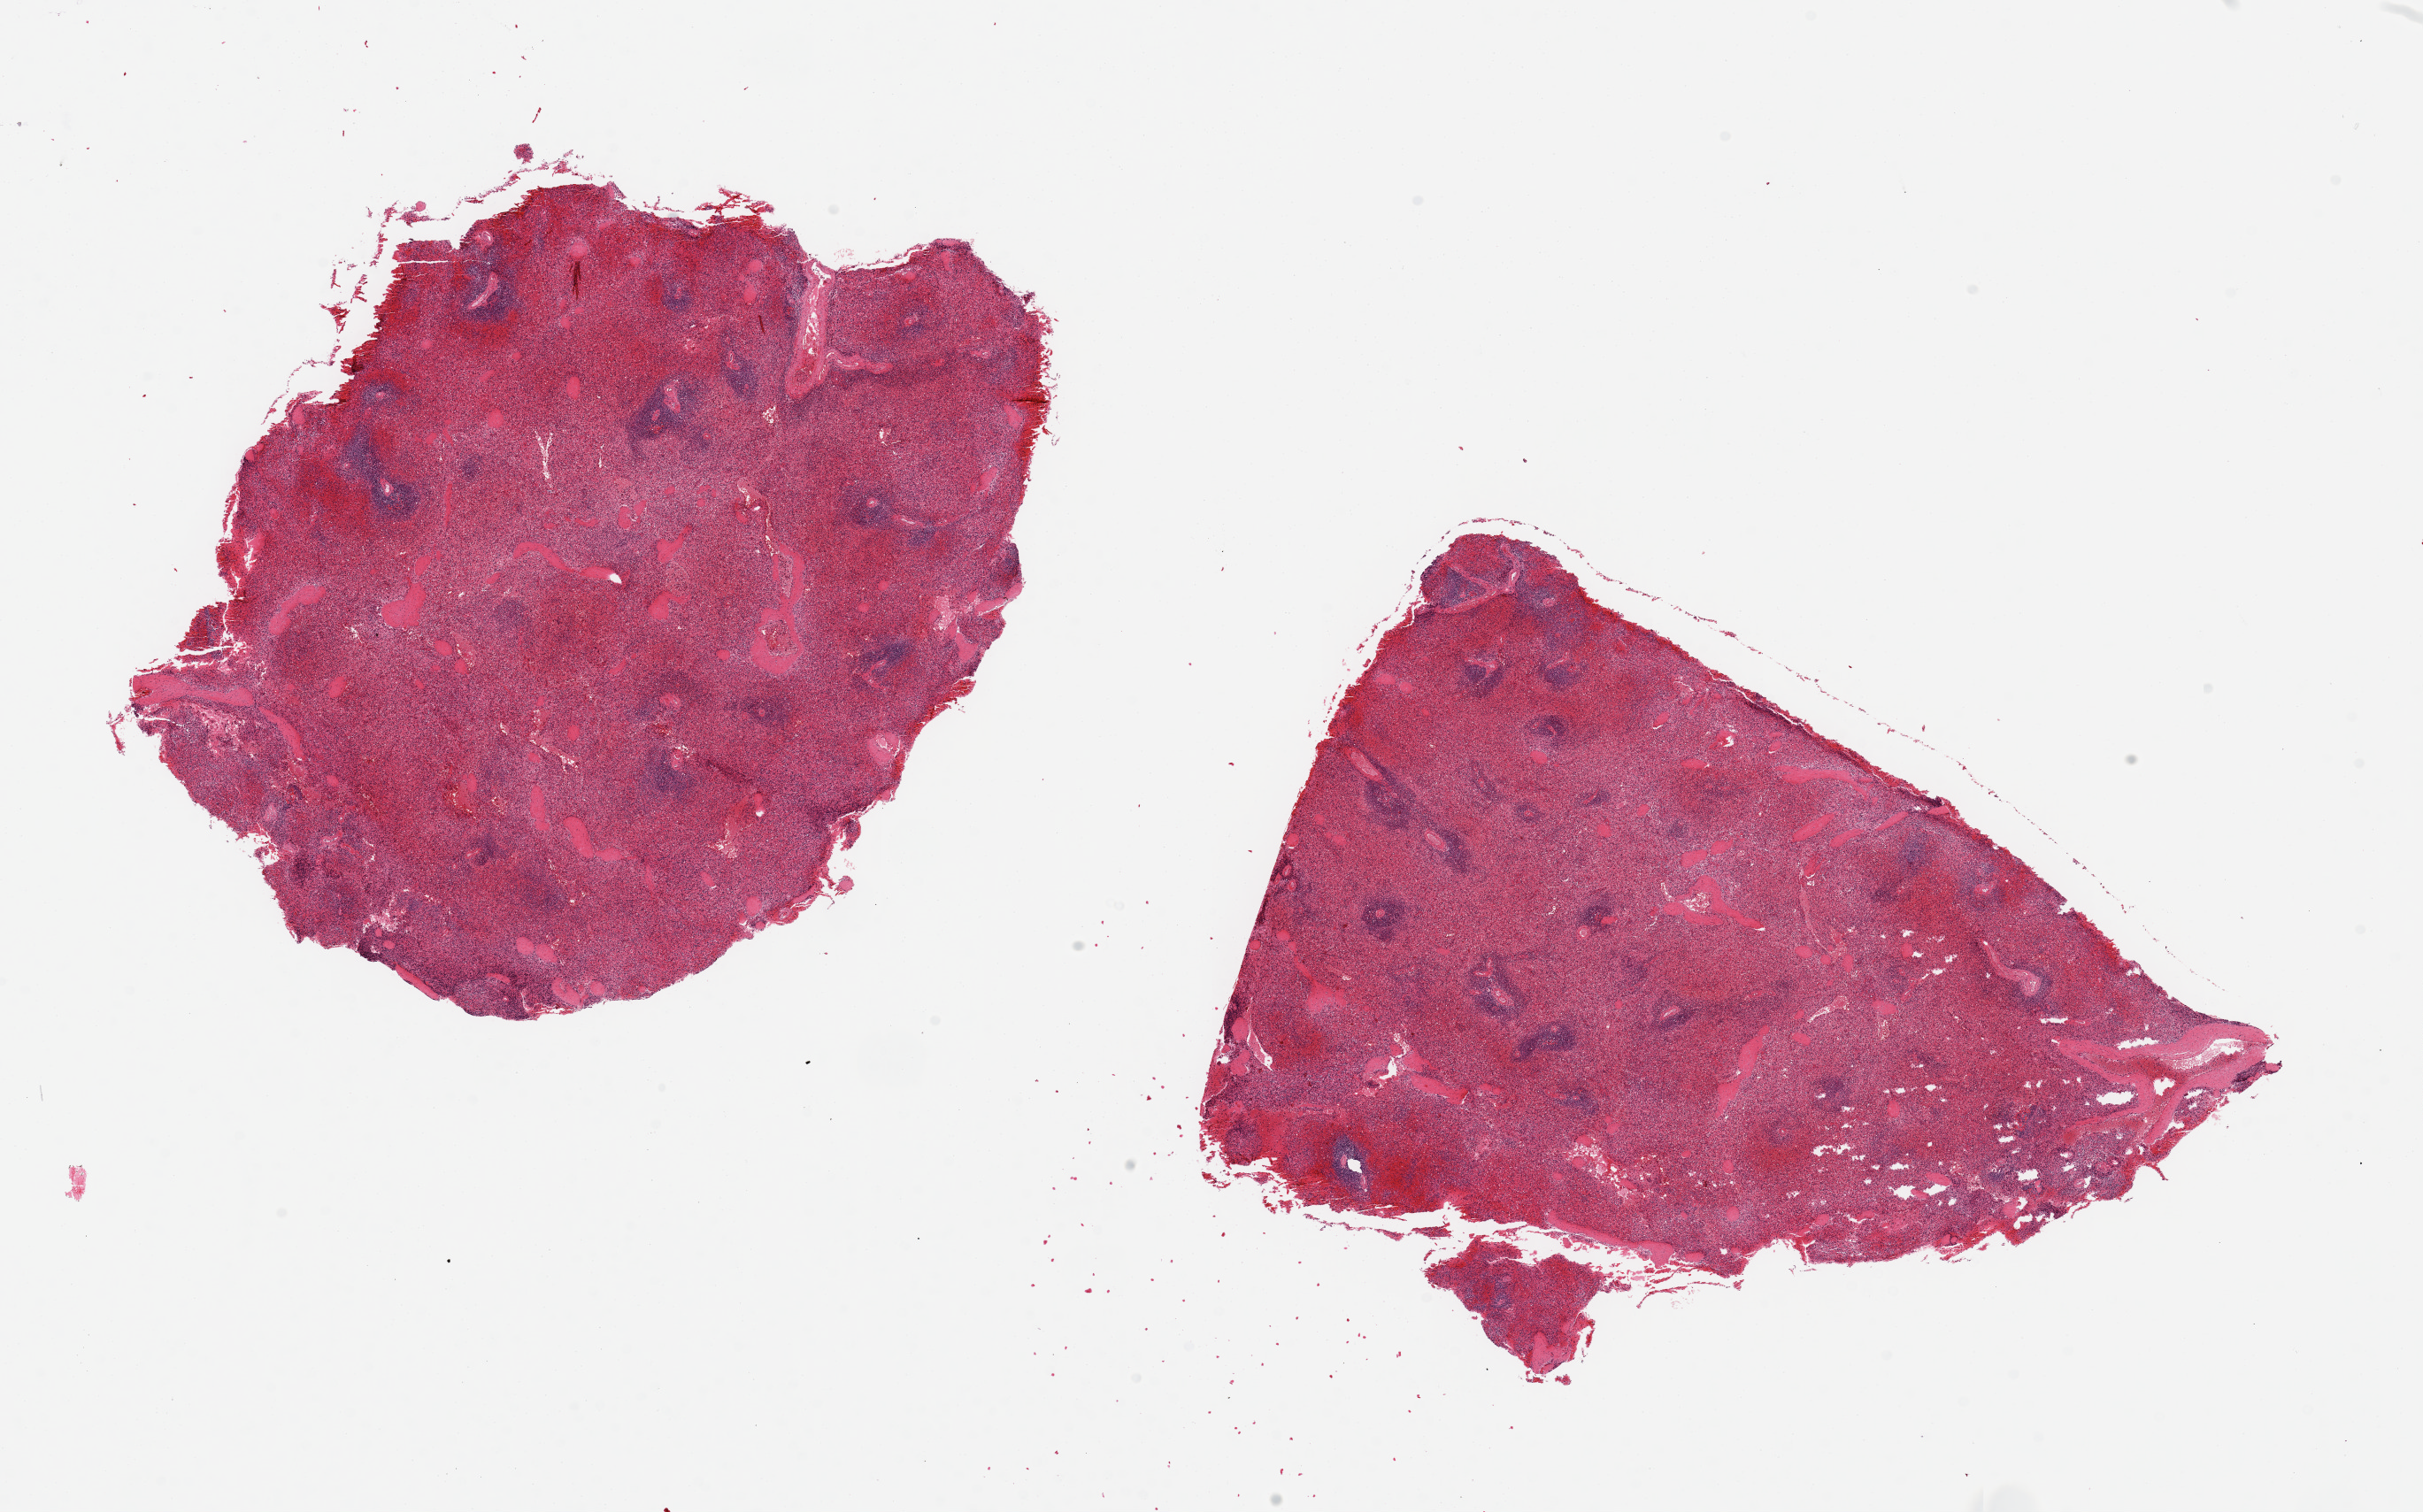
Whole-slide image, hematoxylin and eosin (H&E) stain, brightfield — low-resolution overview of the scanned area, about 21.7 x 13.5 mm (from a 20x scan). PAXgene-fixed, paraffin-embedded tissue. Sampled site (target tissue): spleen. Donor tissue sample. Donor: male.
Reviewer comment on this tissue sample: 2 pieces 8x6 & 8x5 mm; moderately congested.